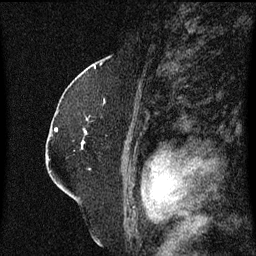
Breast MRI (dynamic contrast-enhanced), one sagittal slice. Position 42 of 60 along the scan axis. Dynamic contrast-enhanced series, image 2 of 3 at this slice position (ordered by acquisition). 1.5 T. TE 4.2 ms, TR 8.4 ms. 2 mm slice thickness. 256 × 256 image matrix, field of view 200 × 200 mm. Female patient, age 52 years. From the clinical record (not read from this slice): setting: breast cancer imaged before/during neoadjuvant chemotherapy; receptor status: HR-positive, HER2-negative.
Annotated regions visible in this slice (semi-automatically segmented with operator editing):
- analysis volume of interest (the breast-tissue region the enhancement analysis was run in; not a lesion): bounding box (x1, y1, x2, y2) in pixels: (82, 118, 90, 149)
- tumour enhancement mask (voxels above the 70 % enhancement threshold inside the analysis volume of interest): (83, 142, 85, 145)